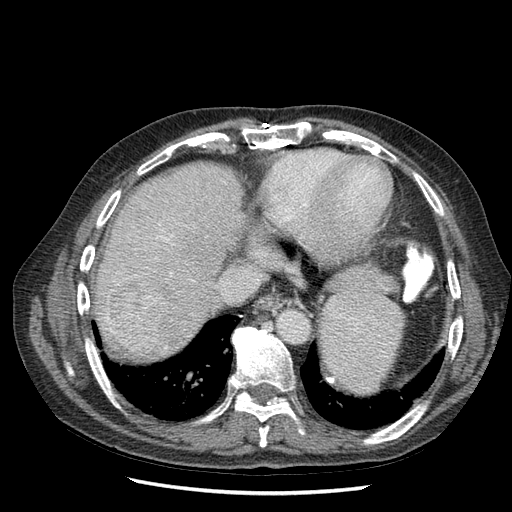
Contrast-enhanced abdominal CT (liver protocol), one axial slice. Position 58 of 67 along the scan axis. Reconstruction kernel STANDARD. 120 kVp. Soft-tissue window (W 400 / L 40 HU). 2.5 mm slice thickness. 512 × 512 image matrix. Case-level facts recorded for this patient, not image findings: diagnosis: hepatocellular carcinoma (patient treated with transarterial chemoembolisation; whether this scan precedes or follows treatment is not stated here); TNM stage (as recorded): Stage-I; Child-Pugh class: A; tumour nodularity: uninodular.
Annotated regions visible in this slice (semi-automatic segmentation, software-assisted and operator-edited):
- abdominal aorta: bounding box <276,308,310,342> (left, top, right, bottom; pixels)
- liver parenchyma outside the tumour (the mass and vessels are separate outlines, so this box may not span the whole liver): <98,162,234,352>
- mass: <111,279,182,350>
- liver vessels: <153,237,163,346>